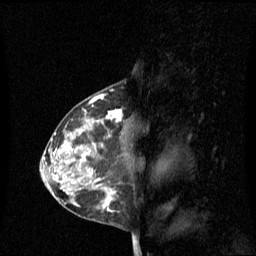
Breast MRI (dynamic contrast-enhanced), one sagittal slice. Slice 37 of 60 in the series (ordered by position). Dynamic contrast-enhanced series, image 2 of 3 at this slice position (ordered by acquisition). 1.5 T. TE 4.2 ms, TR 8.4 ms. 2.1 mm slice thickness. 256 × 256 image matrix. Female patient, age 42 years. Case-level facts recorded for this patient, not image findings: setting: breast cancer imaged before/during neoadjuvant chemotherapy; receptor status: HR-positive, HER2-negative.
Outlined on this slice (semi-automatically segmented with operator editing):
- analysis volume of interest (the breast-tissue region the enhancement analysis was run in; not a lesion): bounding box [x1, y1, x2, y2] px = [68, 110, 127, 201]
- tumour enhancement mask (voxels above the 70 % enhancement threshold inside the analysis volume of interest): [82, 110, 123, 201]